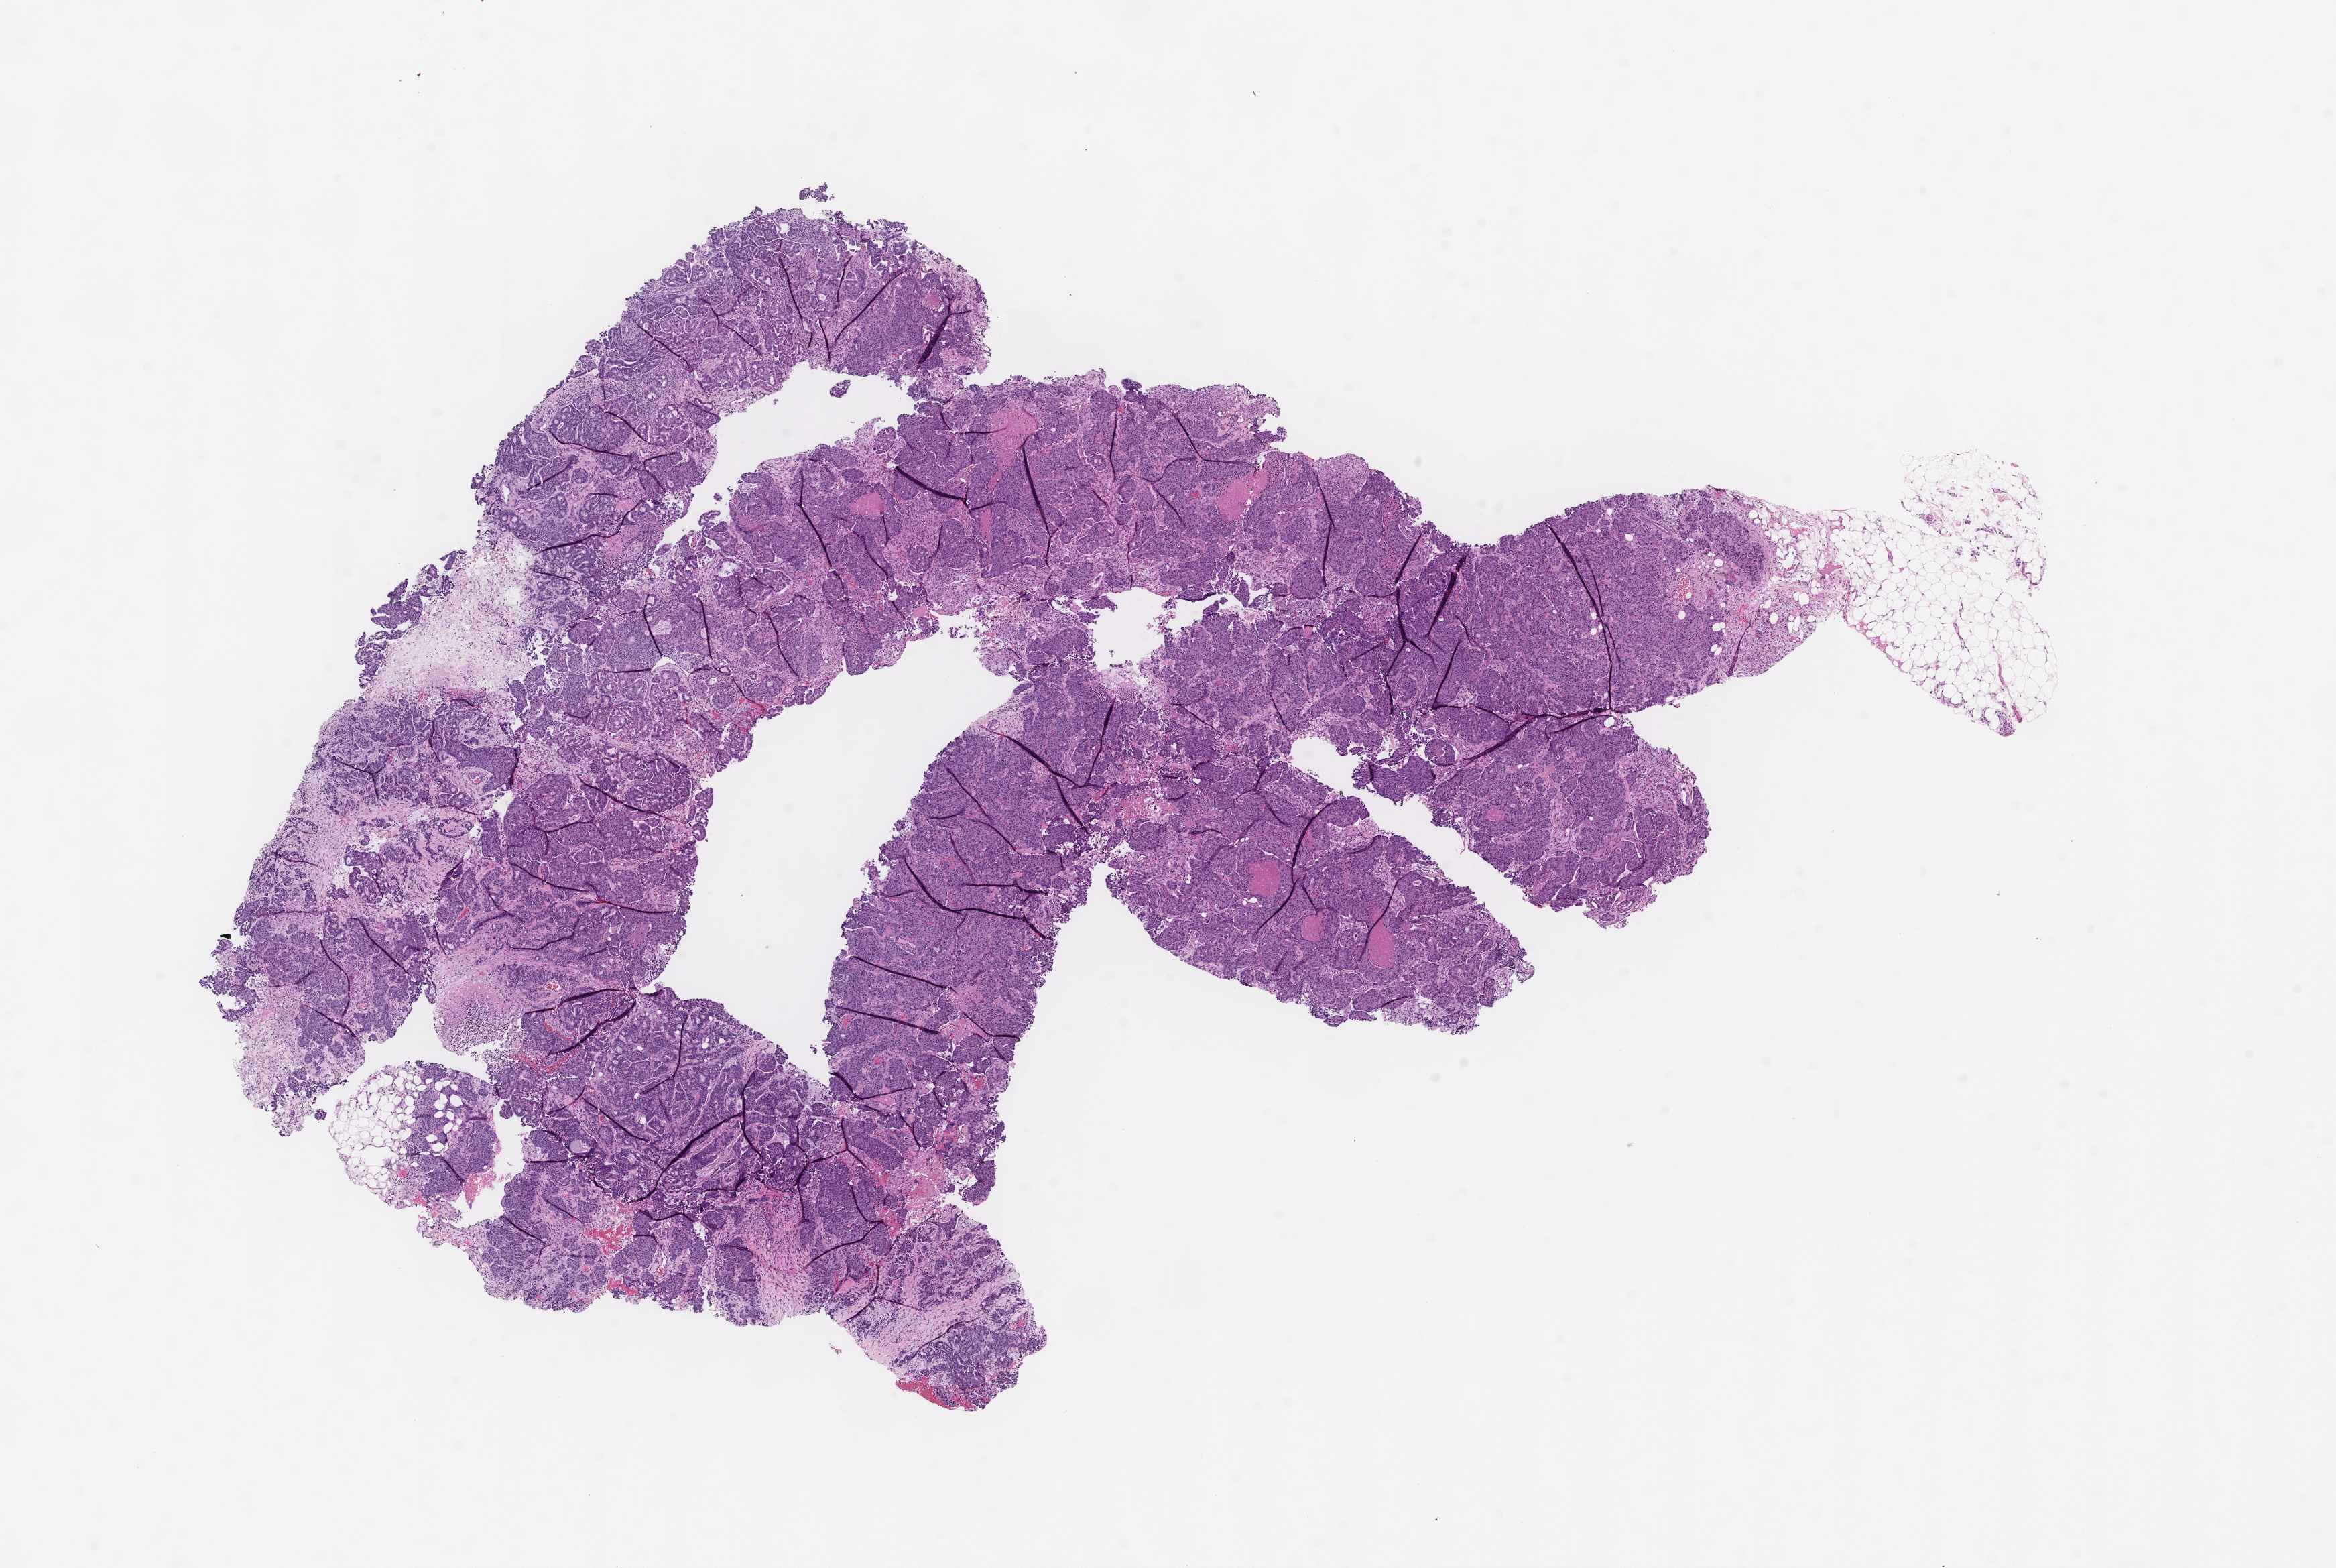
Haematoxylin and eosin whole-slide image, whole scanned area (about 14.1 x 9.4 mm) shown as a low-resolution overview. FFPE section. Site: breast. Specimen time point: archival tissue. Patient: female.
- this section: primary tumour tissue
- diagnosis: Invasive Breast Carcinoma